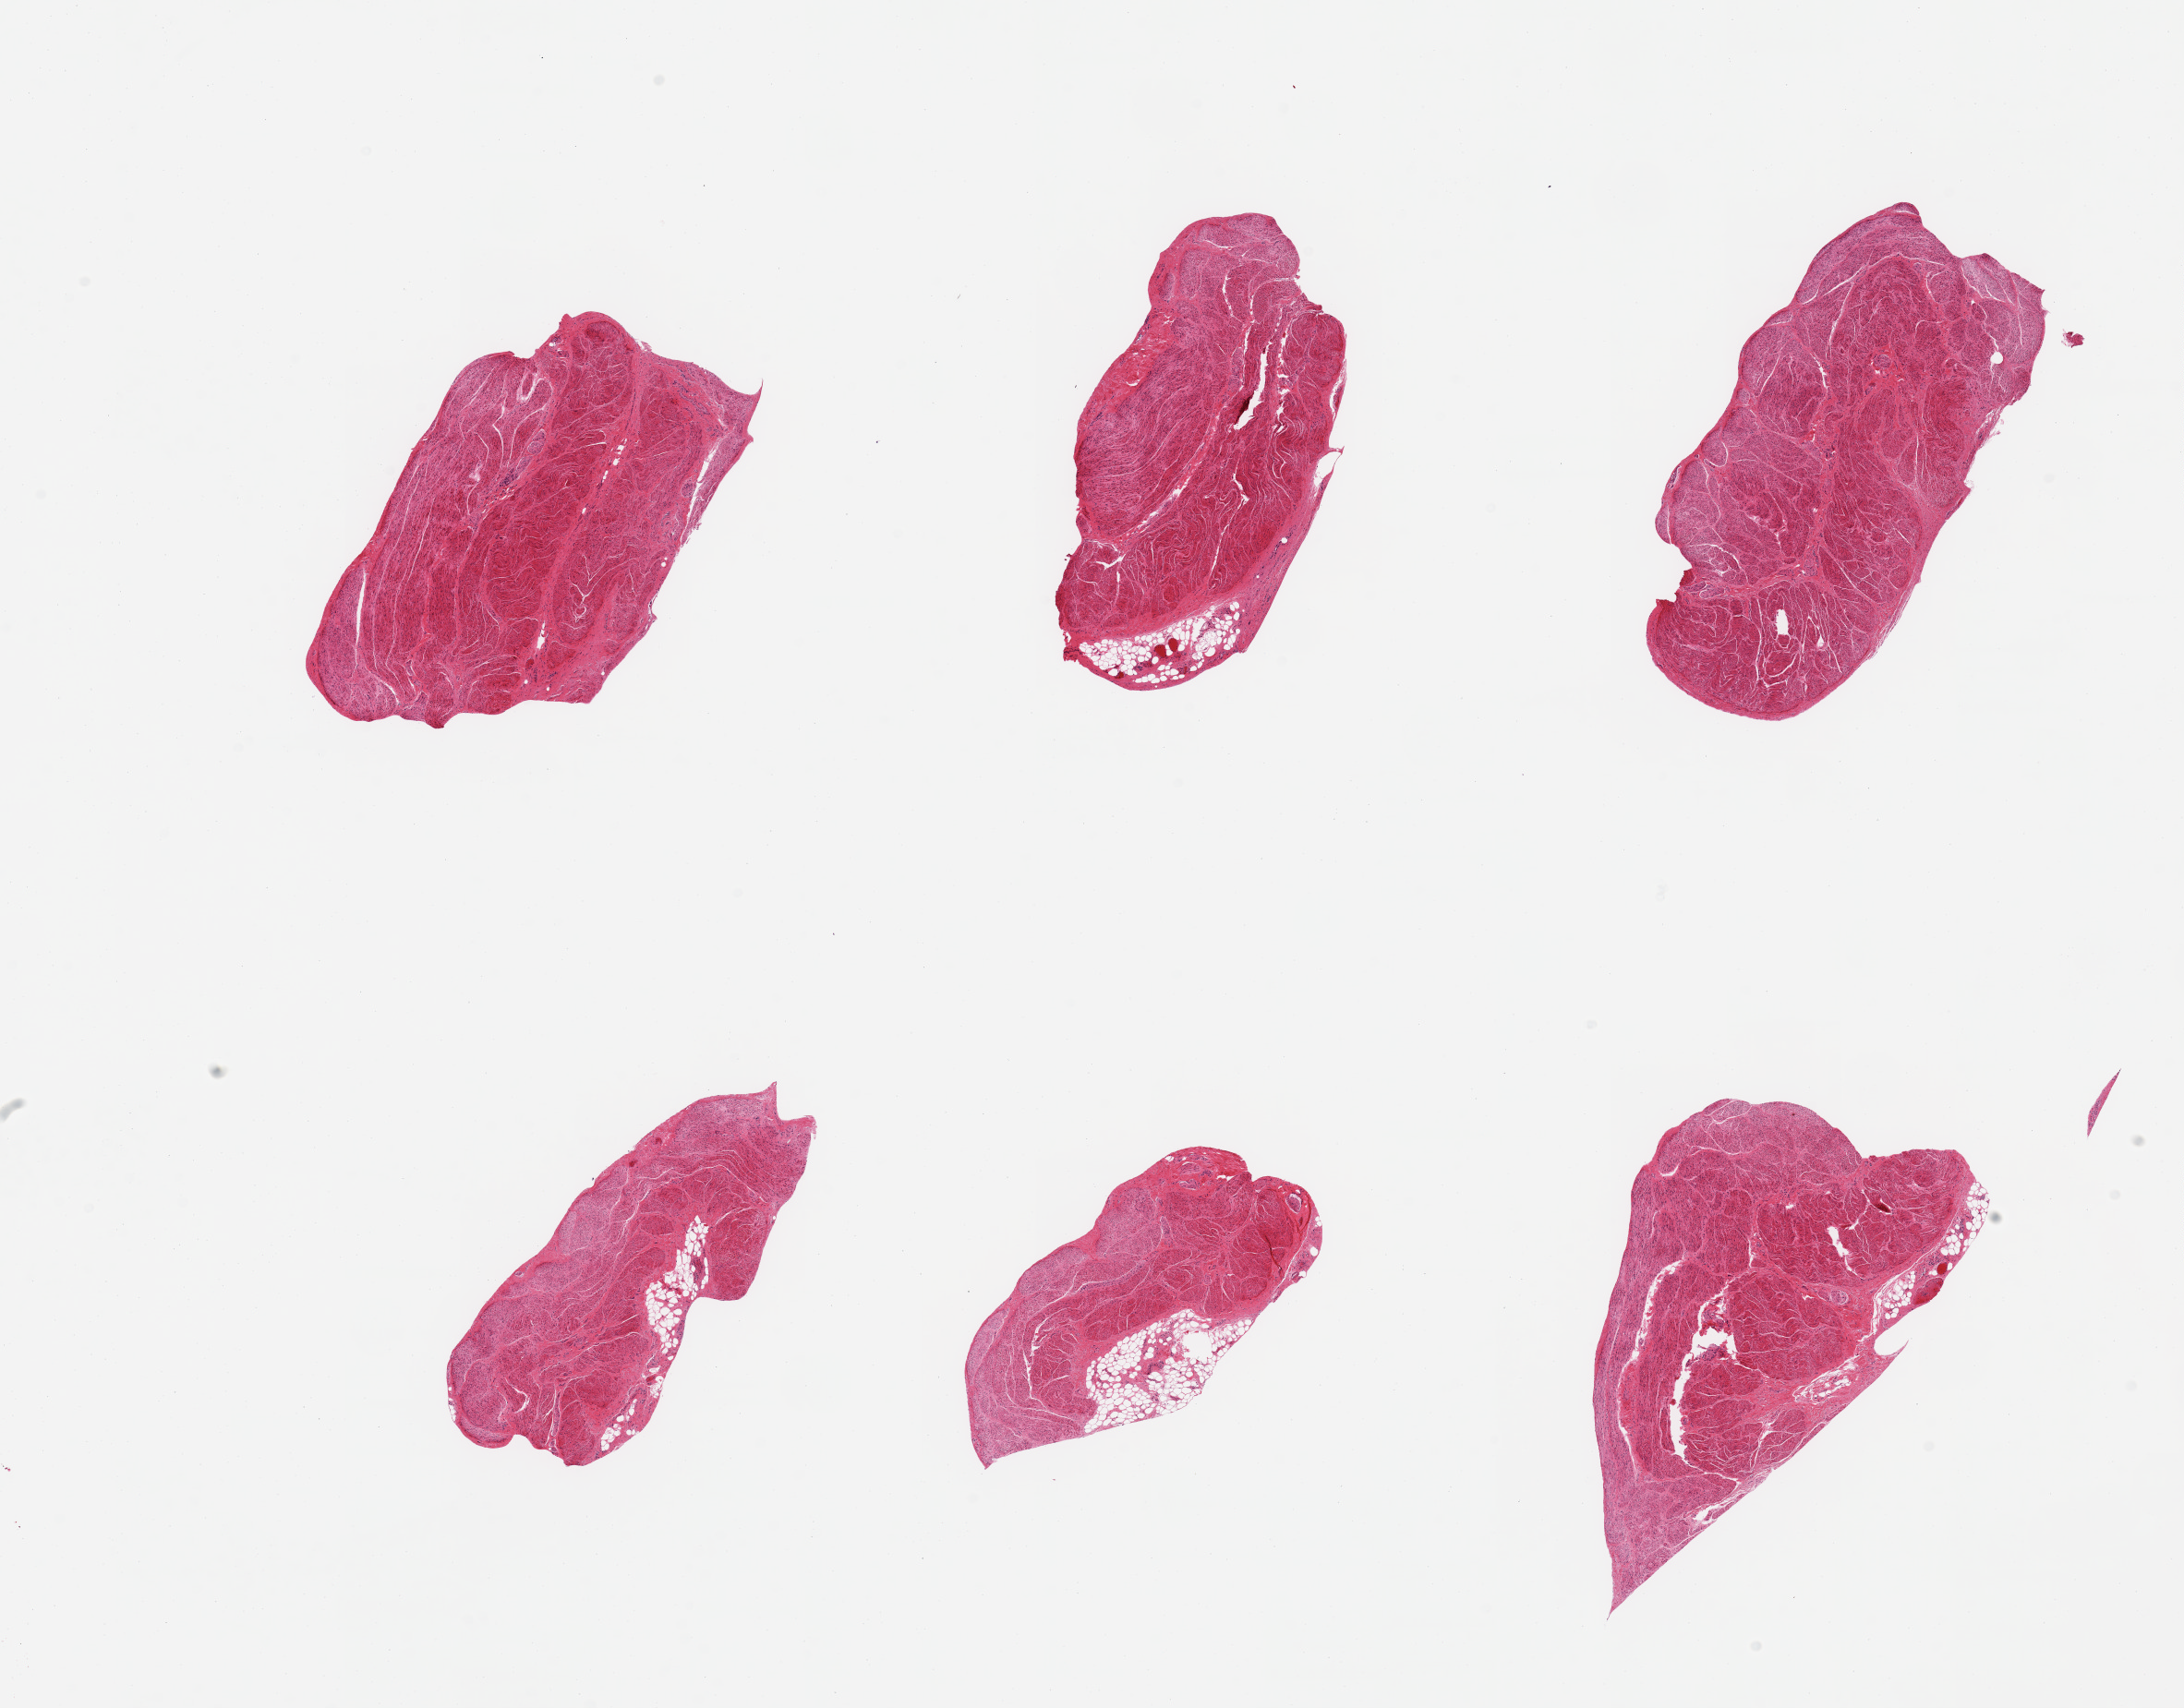
Digitized hematoxylin and eosin (H&E)-stained section, brightfield, shown as a low-resolution overview of the whole scanned area (about 18.7 x 14.6 mm), PAXgene-fixed, paraffin-embedded tissue, target tissue: gastroesophageal junction, donor tissue sample. Female donor.
Pathologist's review note for this sample: 6 pieces; 4 pieces have 10 to 30% fat content.